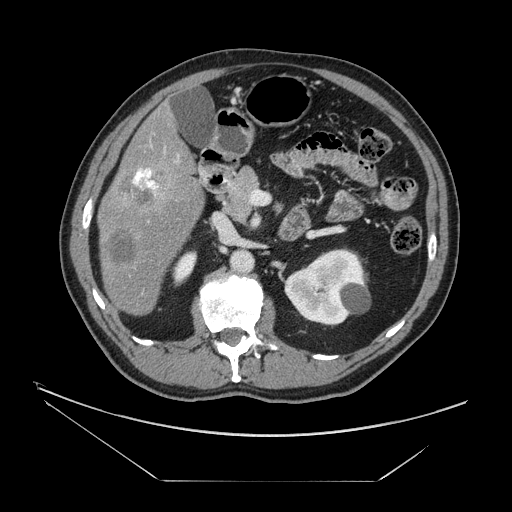
Contrast-enhanced abdominal CT, one axial slice; position 70 of 161 along the scan axis; reconstruction kernel STANDARD; 120 kVp; intravenous contrast given; soft-tissue window (W 400 / L 40 HU); 2.5 mm slice thickness; 512 × 512 image matrix, field of view 440 × 440 mm. Male patient, age 65 years. Case-level facts recorded for this patient, not image findings: diagnosis: colorectal cancer liver metastases, imaged before liver resection; multiple liver metastases: yes; largest metastasis: 4.2 cm; disease in both lobes: yes.
Outlined on this slice (manually delineated by an expert):
- liver: bounding box (x1, y1, x2, y2) in pixels: (100, 107, 204, 315)
- portal vein (with intrahepatic branches): (134, 158, 179, 195)
- liver metastasis: (110, 233, 139, 266)
- liver metastasis: (118, 166, 167, 208)